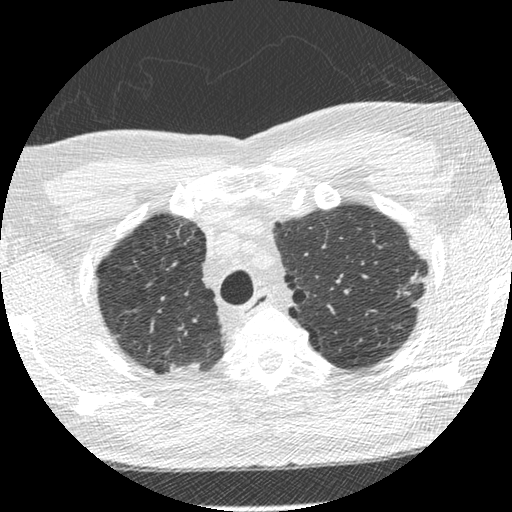
Low-dose screening chest CT, one axial slice; position 235 of 275 along the scan axis; reconstruction kernel STANDARD; 120 kVp; lung window (W 1500 / L -600 HU); 512 × 512 image matrix, field of view 330 × 330 mm.
Annotated regions visible in this slice (expert manual segmentation):
- lesion 1 (tumor, upper lobe of left lung): bounding box [x1, y1, x2, y2] px = [411, 272, 422, 284]